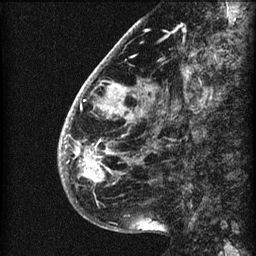
Breast MRI (dynamic contrast-enhanced), one sagittal slice. Position 18 of 60 along the scan axis. 3 images stored at this slice position (order not interpretable as contrast timing). 1.5 T. TE 4.2 ms, TR 22.7 ms. 256 × 256 image matrix. Patient: female, 48 years. From the clinical record (not read from this slice): setting: breast cancer imaged before/during neoadjuvant chemotherapy; receptor status: triple-negative.
Annotated regions visible in this slice (semi-automatic segmentation, software-assisted and operator-edited):
- analysis volume of interest (the breast-tissue region the enhancement analysis was run in; not a lesion): bounding box (x1, y1, x2, y2) in pixels: (58, 30, 173, 207)
- tumour enhancement mask (voxels above the 90 % enhancement threshold inside the analysis volume of interest): (60, 82, 129, 178)